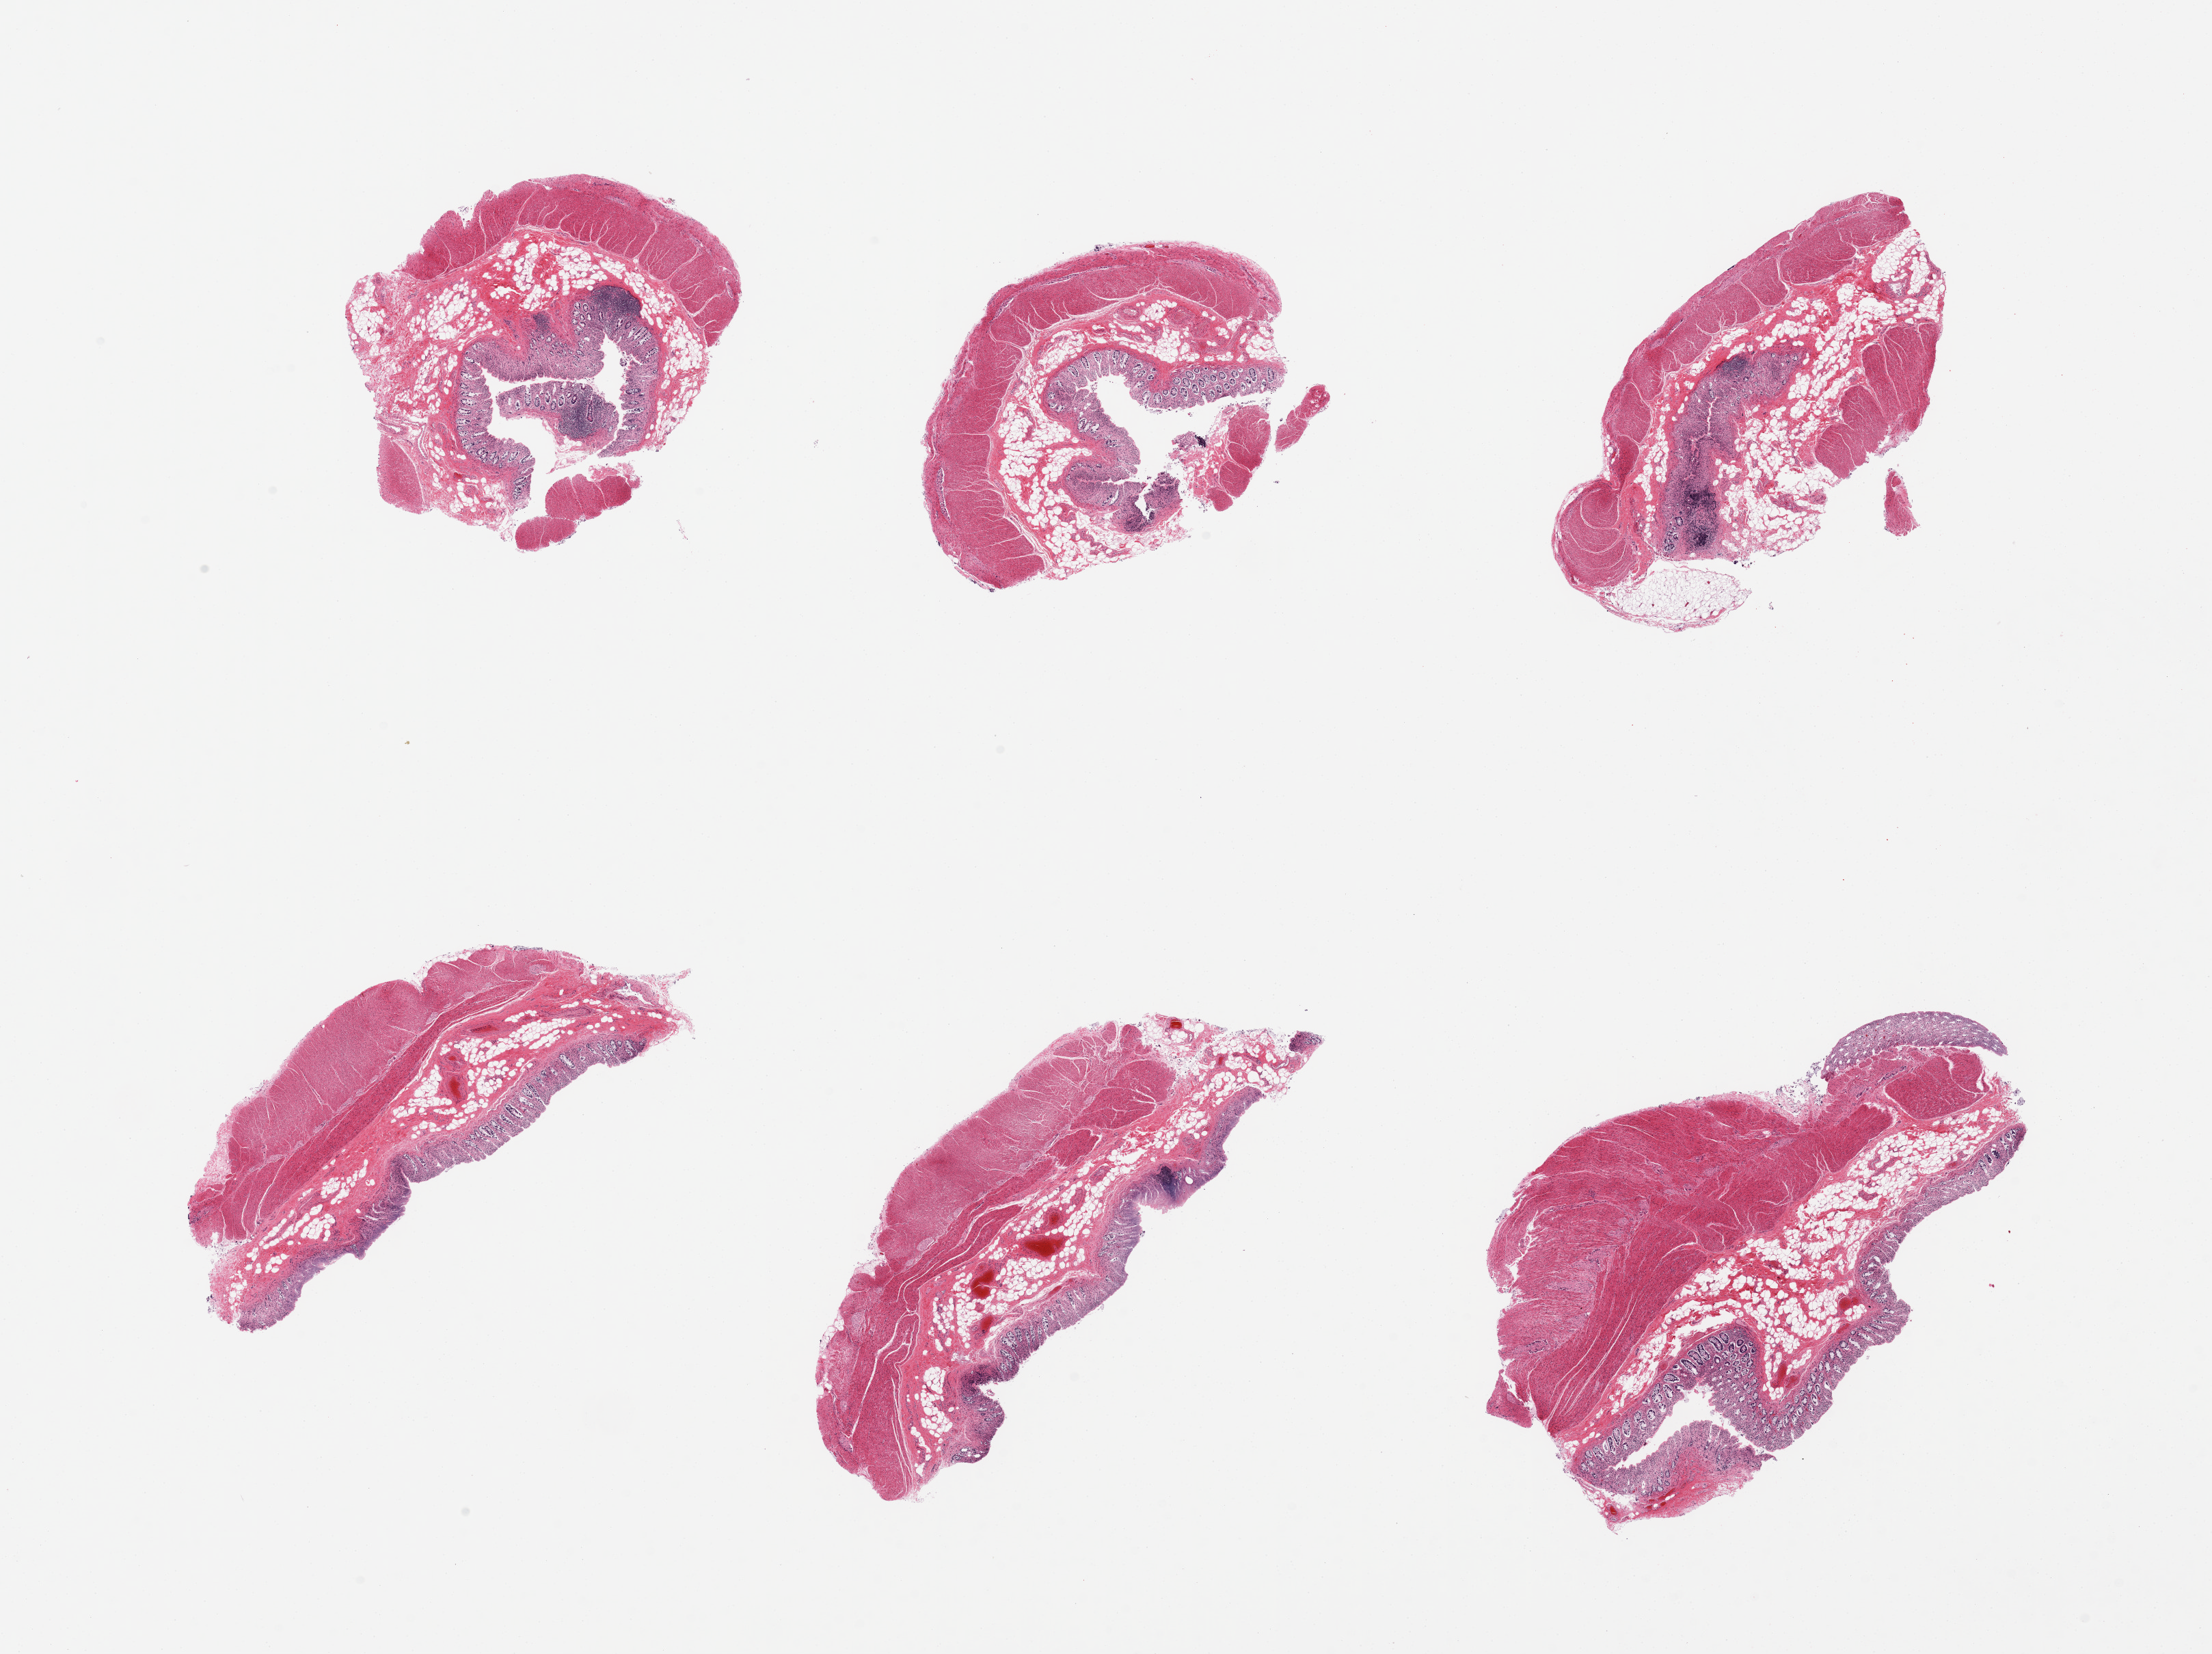
H&E whole-slide image — a low-resolution overview of the entire scanned area, about 25.6 x 19.1 mm. PAXgene-fixed, paraffin-embedded tissue. Target tissue: sigmoid colon. Donor tissue sample. Donor: male.
Review note (as recorded): 6 pieces, muscularis (target) and severely autolyzed mucosa (not target).